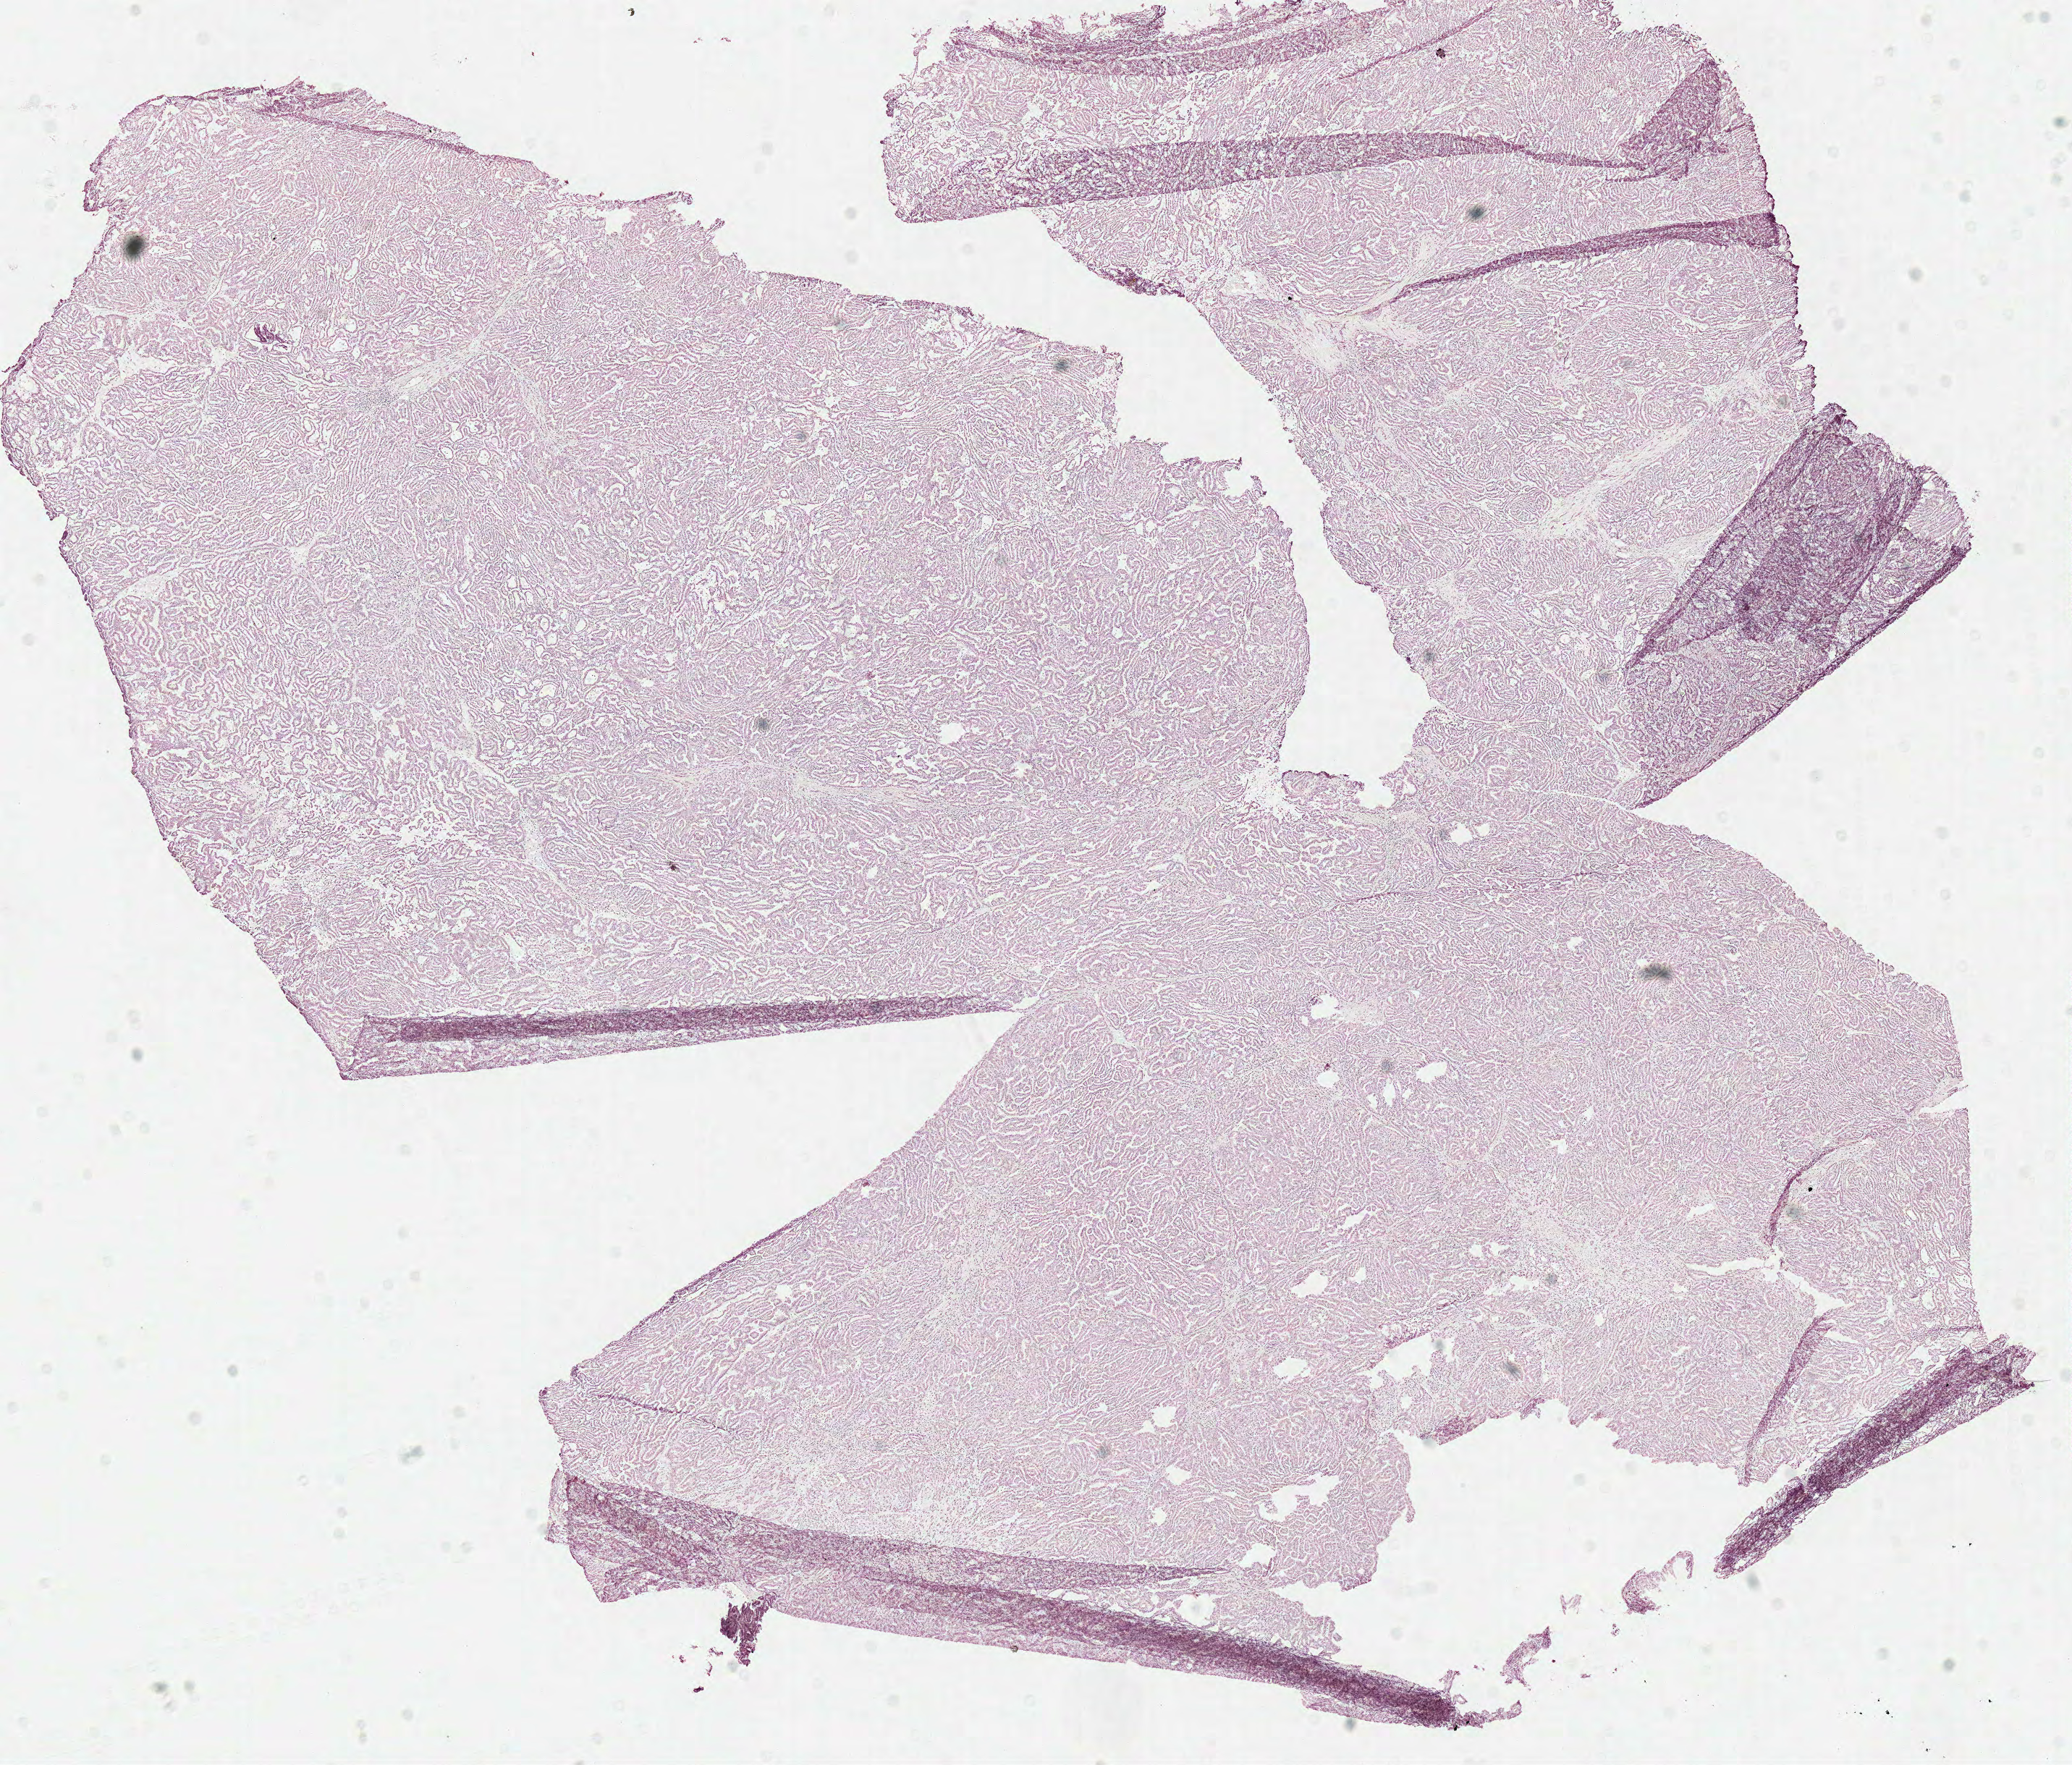
H&E whole-slide image, a low-resolution overview of the entire scanned area, about 11.3 x 9.6 mm, frozen section from the top of the tissue portion, primary tumour sample from the kidney. Male, age 46 years at initial diagnosis. Slide review estimates, as recorded: tumour cells 100%, tumour nuclei 90%, normal cells 0%, stromal cells 0%, necrosis 0%.
* pathologic diagnosis: Papillary adenocarcinoma, NOS
* laterality: left
* AJCC pathologic stage: III (7th edition)